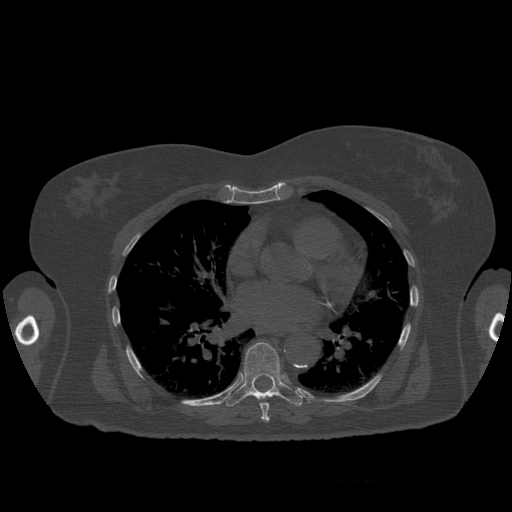
CT including the spine, one axial slice; position 384 of 399 along the scan axis; reconstruction kernel STANDARD; 120 kVp; bone window (W 1800 / L 400 HU); 1.25 mm slice thickness; 512 × 512 image matrix. Patient age 81 years. From the clinical record (not read from this slice): primary cancer: renal.
Structures marked on this image (semi-automatically segmented with operator editing):
- T7 vertebra: bounding box <258,398,270,422> (left, top, right, bottom; pixels)
- T8 vertebra: <225,342,303,407>